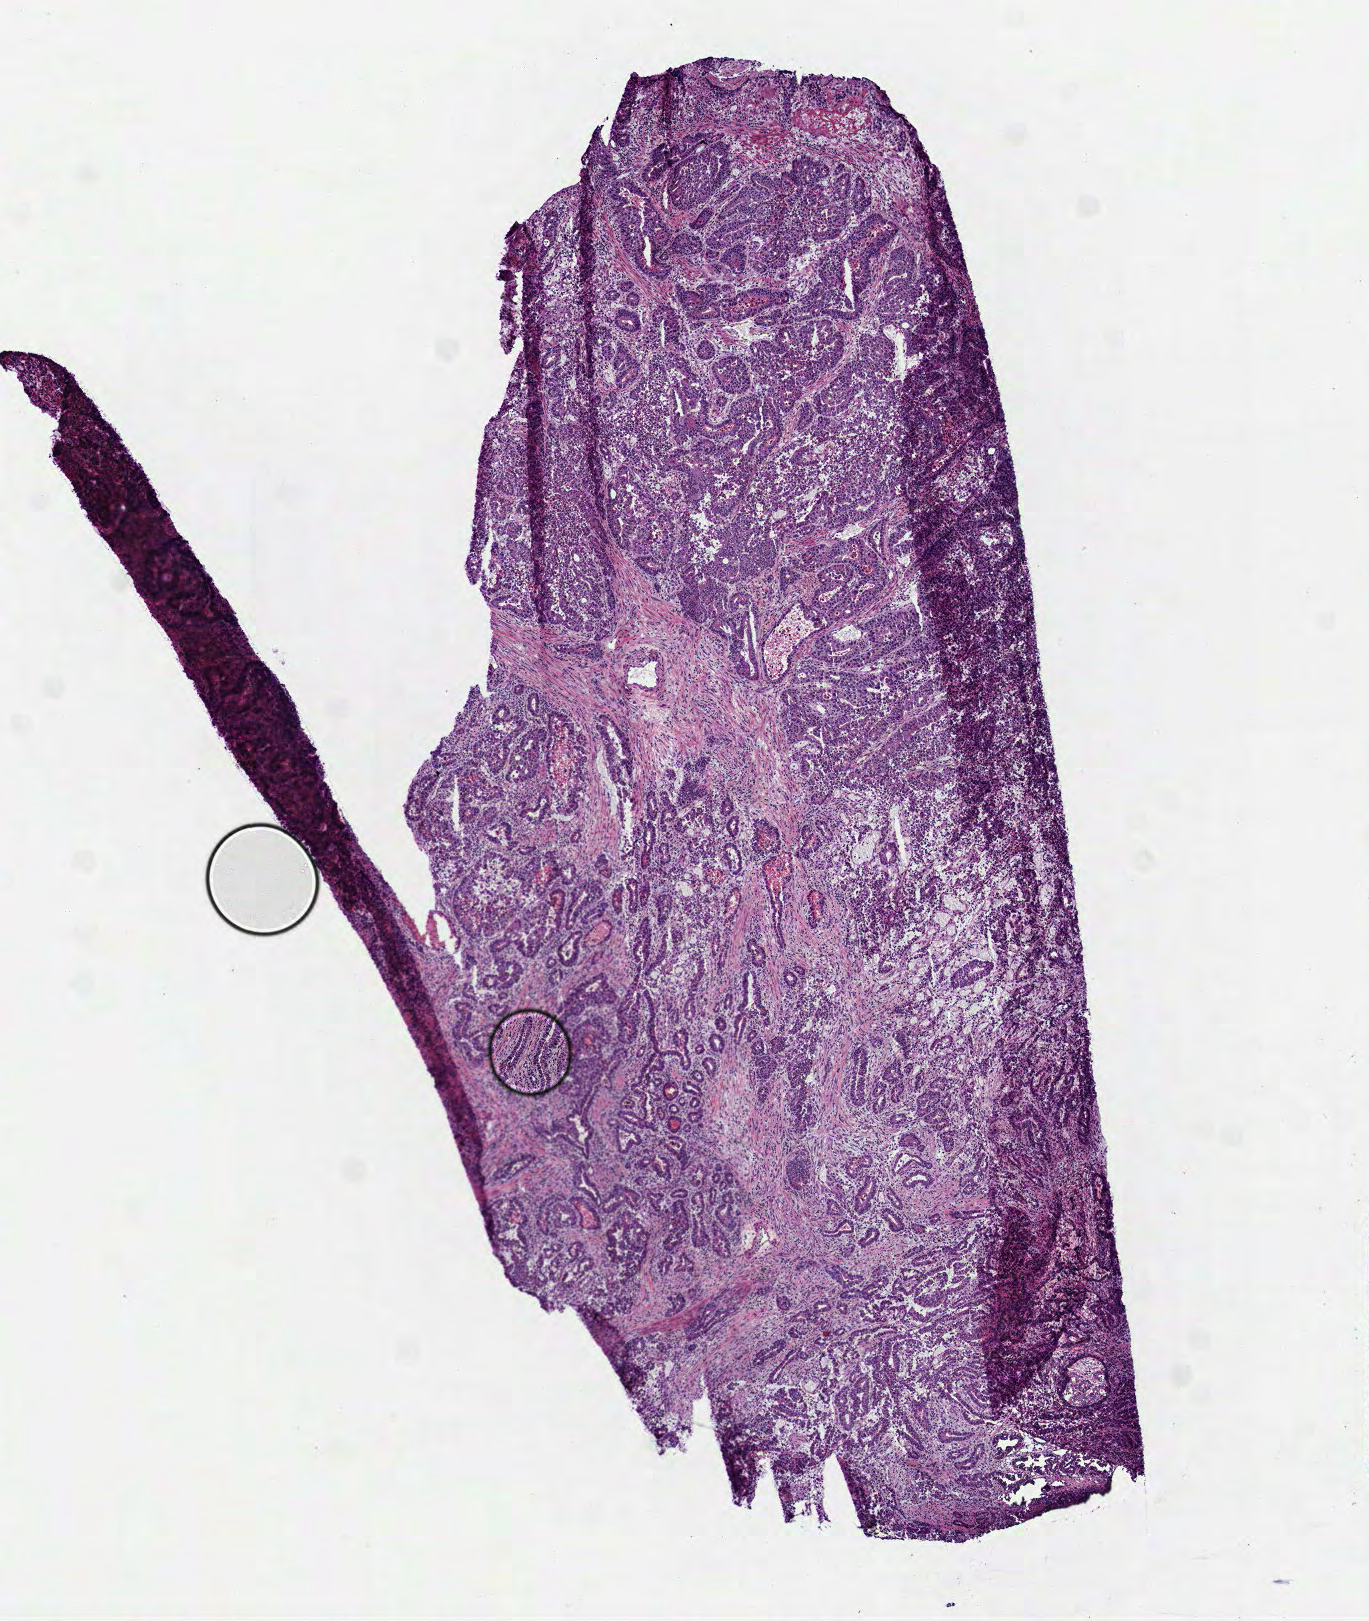
Whole-slide histology image, H&E, whole scanned area (about 5.5 x 6.5 mm, from a 40x scan) shown as a low-resolution overview. Frozen section from the top of the tissue portion. Sample: primary tumour, stomach. Patient: male, age at initial diagnosis 74 years. Histologic grade: G2 (moderately differentiated). Slide review estimates, as recorded: tumour cells 100%, tumour nuclei 80%, normal cells 0%, stromal cells 0%, necrosis 0%. Inflammatory infiltration, as recorded: lymphocyte infiltration 10%, monocyte infiltration 0%, neutrophil infiltration 0%.
AJCC pathologic stage: IIIB (7th edition). Lymph nodes positive (case pathology): 4 of 49 examined. Pathologic diagnosis: Signet ring cell carcinoma (cardia, NOS).